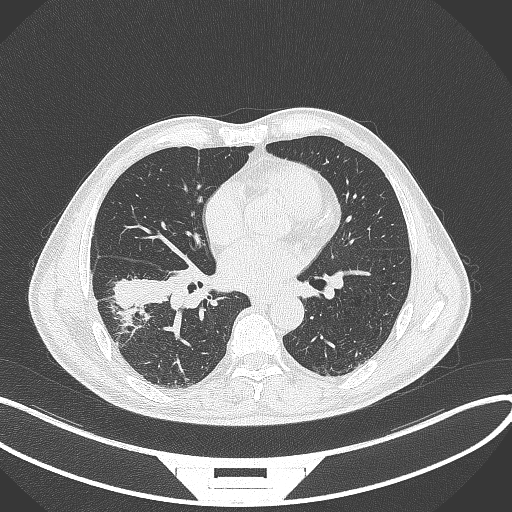
Chest CT, one axial slice; position 166 of 364 along the scan axis; 120 kVp; lung window (W 1500 / L -600 HU); 512 × 512 image matrix, field of view 400 × 400 mm. Male patient, age 58 years. From the clinical record (not read from this slice): clinical TNM (as recorded): T3 N0 M0.
Annotated regions visible in this slice (rectangle marked by the reading radiologist):
- lung tumour (recorded histology: squamous cell carcinoma): box from (x=112, y=275) to (x=173, y=311) px